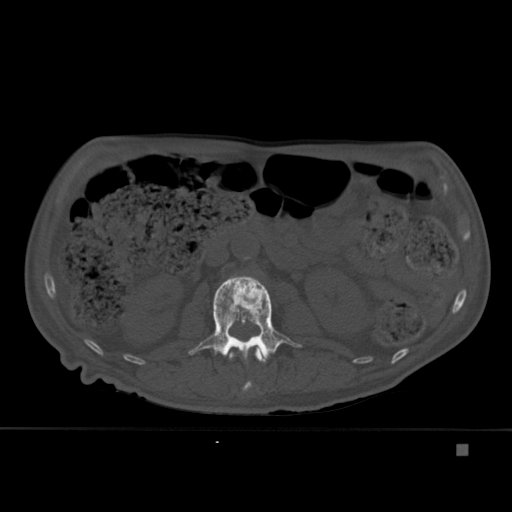
CT including the spine, one axial slice; slice 164 of 451 in the series (ordered by position); bone window (W 1800 / L 400 HU); 1.5 mm slice thickness; 512 × 512 image matrix, field of view 378 × 378 mm. Male patient, age 75 years. From the clinical record (not read from this slice): primary cancer: prostate.
Annotated regions visible in this slice (semi-automatic segmentation, software-assisted and operator-edited):
- L1 vertebra: bounding box (x1, y1, x2, y2) in pixels: (229, 348, 266, 391)
- L2 vertebra: (188, 275, 302, 364)